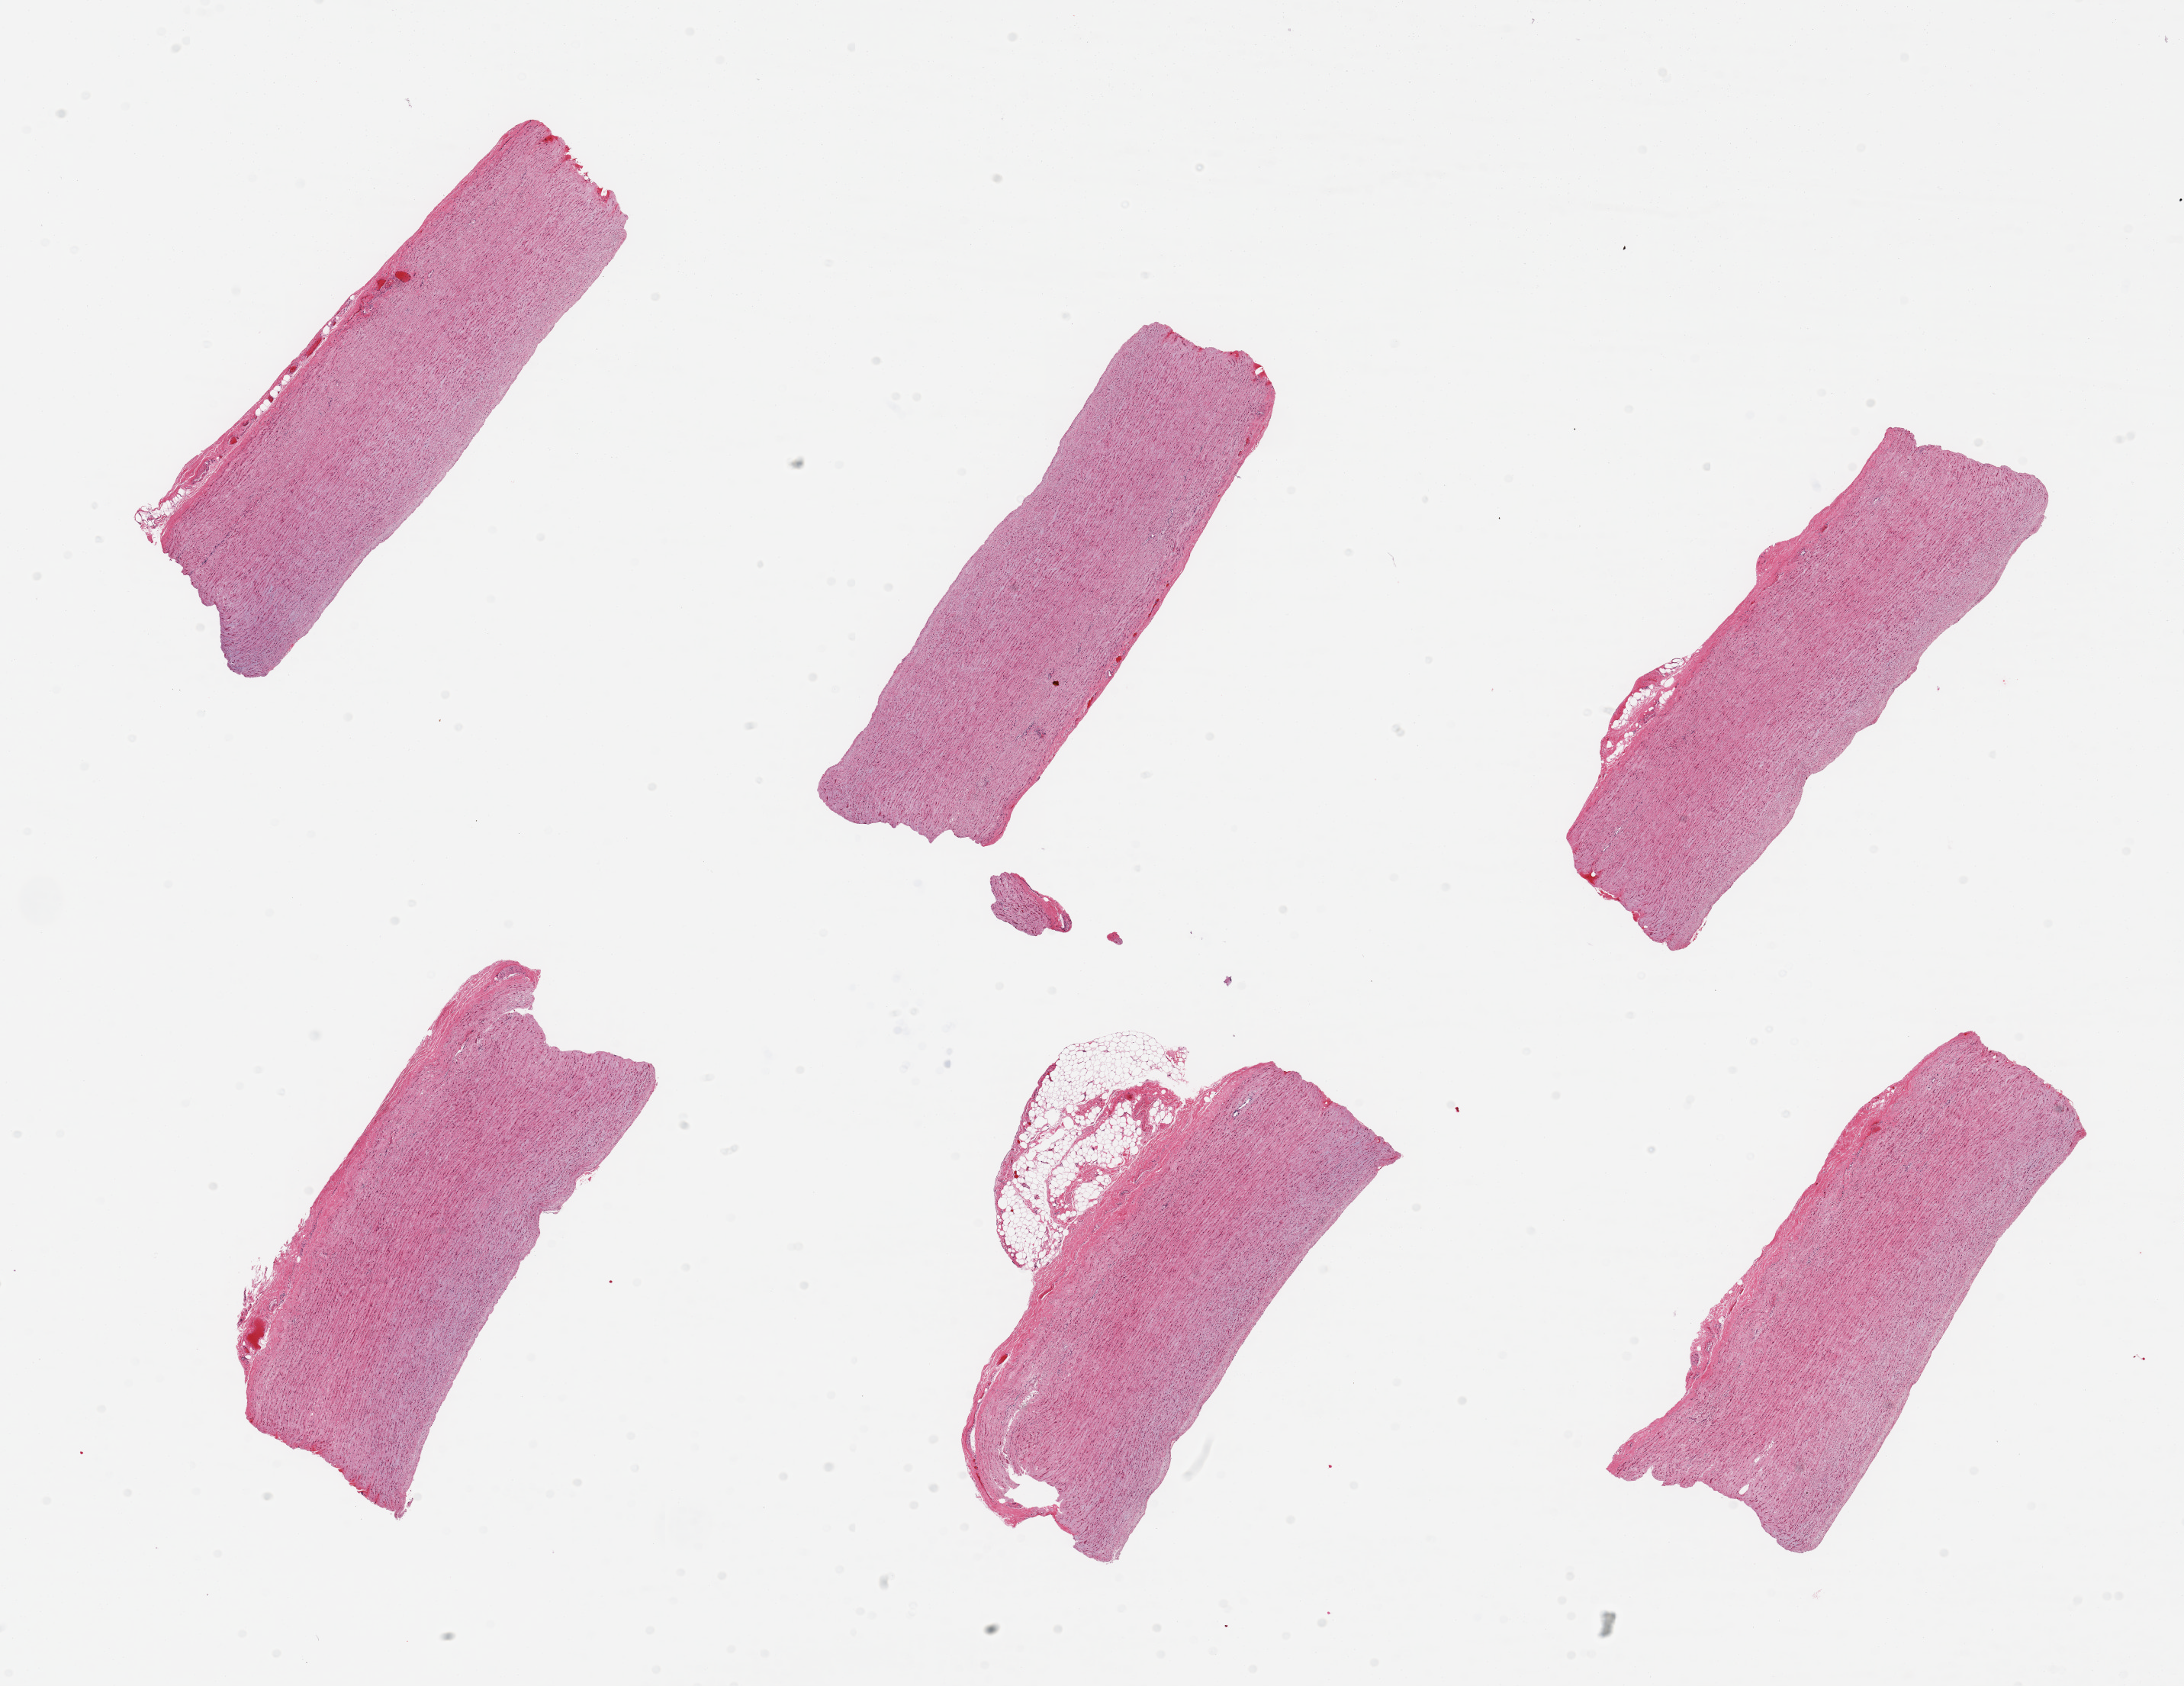
H&E whole-slide image — whole scanned area (about 22.6 x 17.5 mm) shown as a low-resolution overview. PAXgene-fixed paraffin-embedded (PFPE) section. Section of aorta (target tissue). Donor tissue sample. Donor: male.
Pathologist's review note for this sample: 6 pieces, trace atherosis.